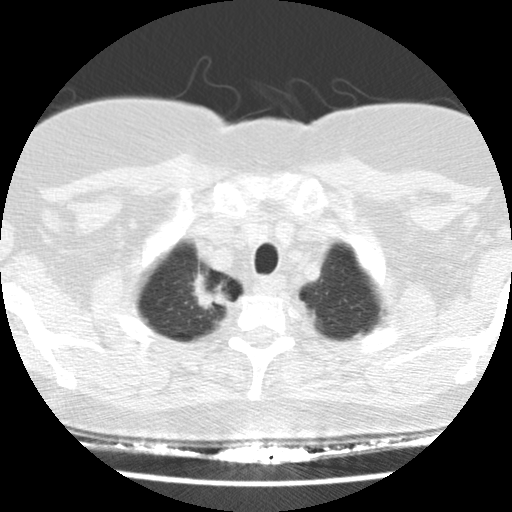
Chest CT (low-dose screening protocol), one axial image. Baseline screening round. Lung window (W 1500 / L -600 HU). Standard (soft-tissue) reconstruction kernel (STANDARD). 120 kVp. Slice 14 of 148 in the series. 512 × 512 image matrix. Female participant, aged 58 years at enrolment. Former smoker at enrolment.
Expert reader's lesion annotation, bounding box [x1, y1, x2, y2] px = [168, 255, 246, 332]. The exam's reader record, not a measurement of the box and not confirmed to be the same lesion: non-calcified nodule or mass ≥4 mm, right upper lobe, 28 × 24 mm, spiculated (stellate) margins, soft tissue attenuation. Lung cancer was diagnosed 40 days after this screen: adenocarcinoma, NOS, right upper lobe, poorly differentiated (G3), stage IB (AJCC 6th edition), 29 mm at pathology.